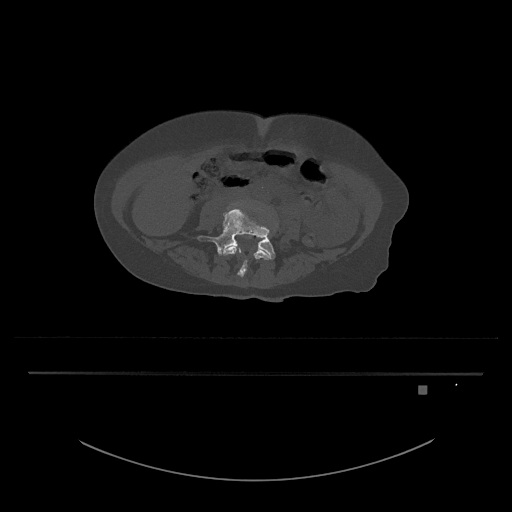
CT including the spine, one axial slice; slice 328 of 797 in the series (ordered by position); bone window (W 1800 / L 400 HU); 0.5 mm slice thickness; 512 × 512 image matrix, field of view 500 × 500 mm. Female patient, age 57 years. From the clinical record (not read from this slice): primary cancer: cervical.
Structures marked on this image (semi-automatic segmentation, software-assisted and operator-edited):
- L4 vertebra: bounding box (x1, y1, x2, y2) in pixels: (223, 245, 271, 277)